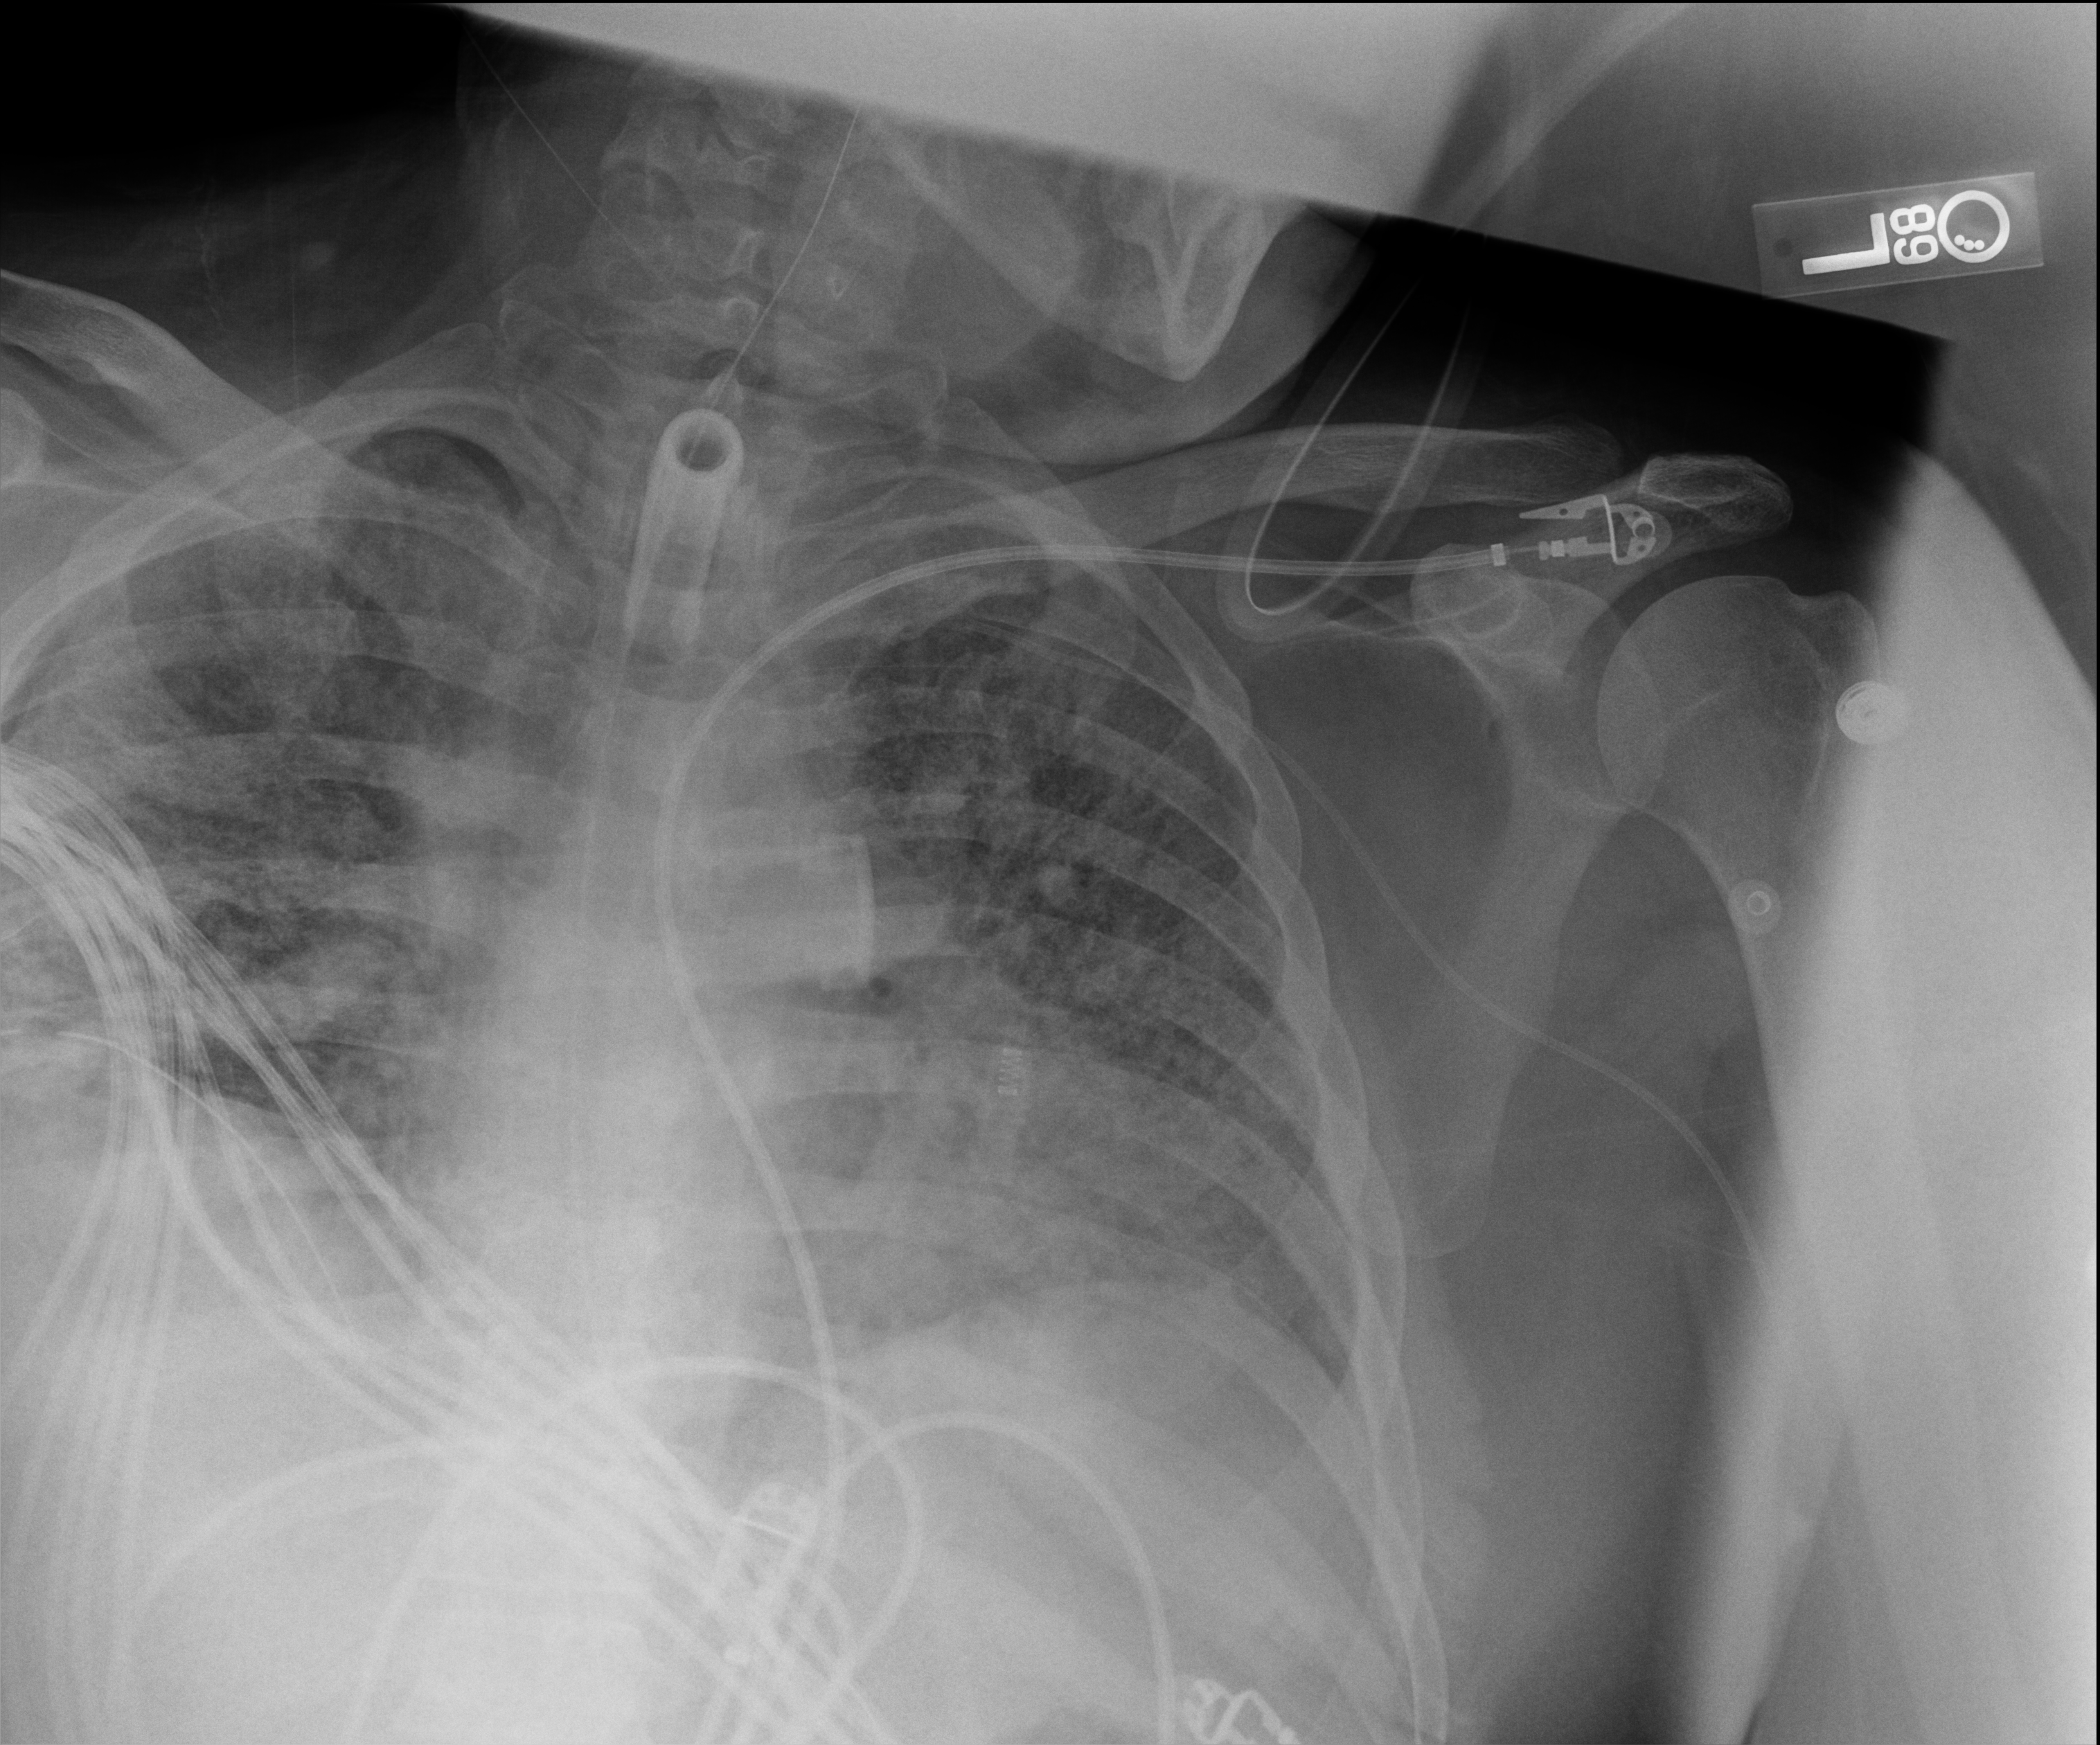
Chest radiograph; anteroposterior (AP) projection. Patient hospitalised with COVID-19; male, aged 18–59 years.
Hospital-stay facts (about this admission, not read from this image; timing relative to this image not recorded): diabetes (admission record): no; length of hospital stay: 80 days.